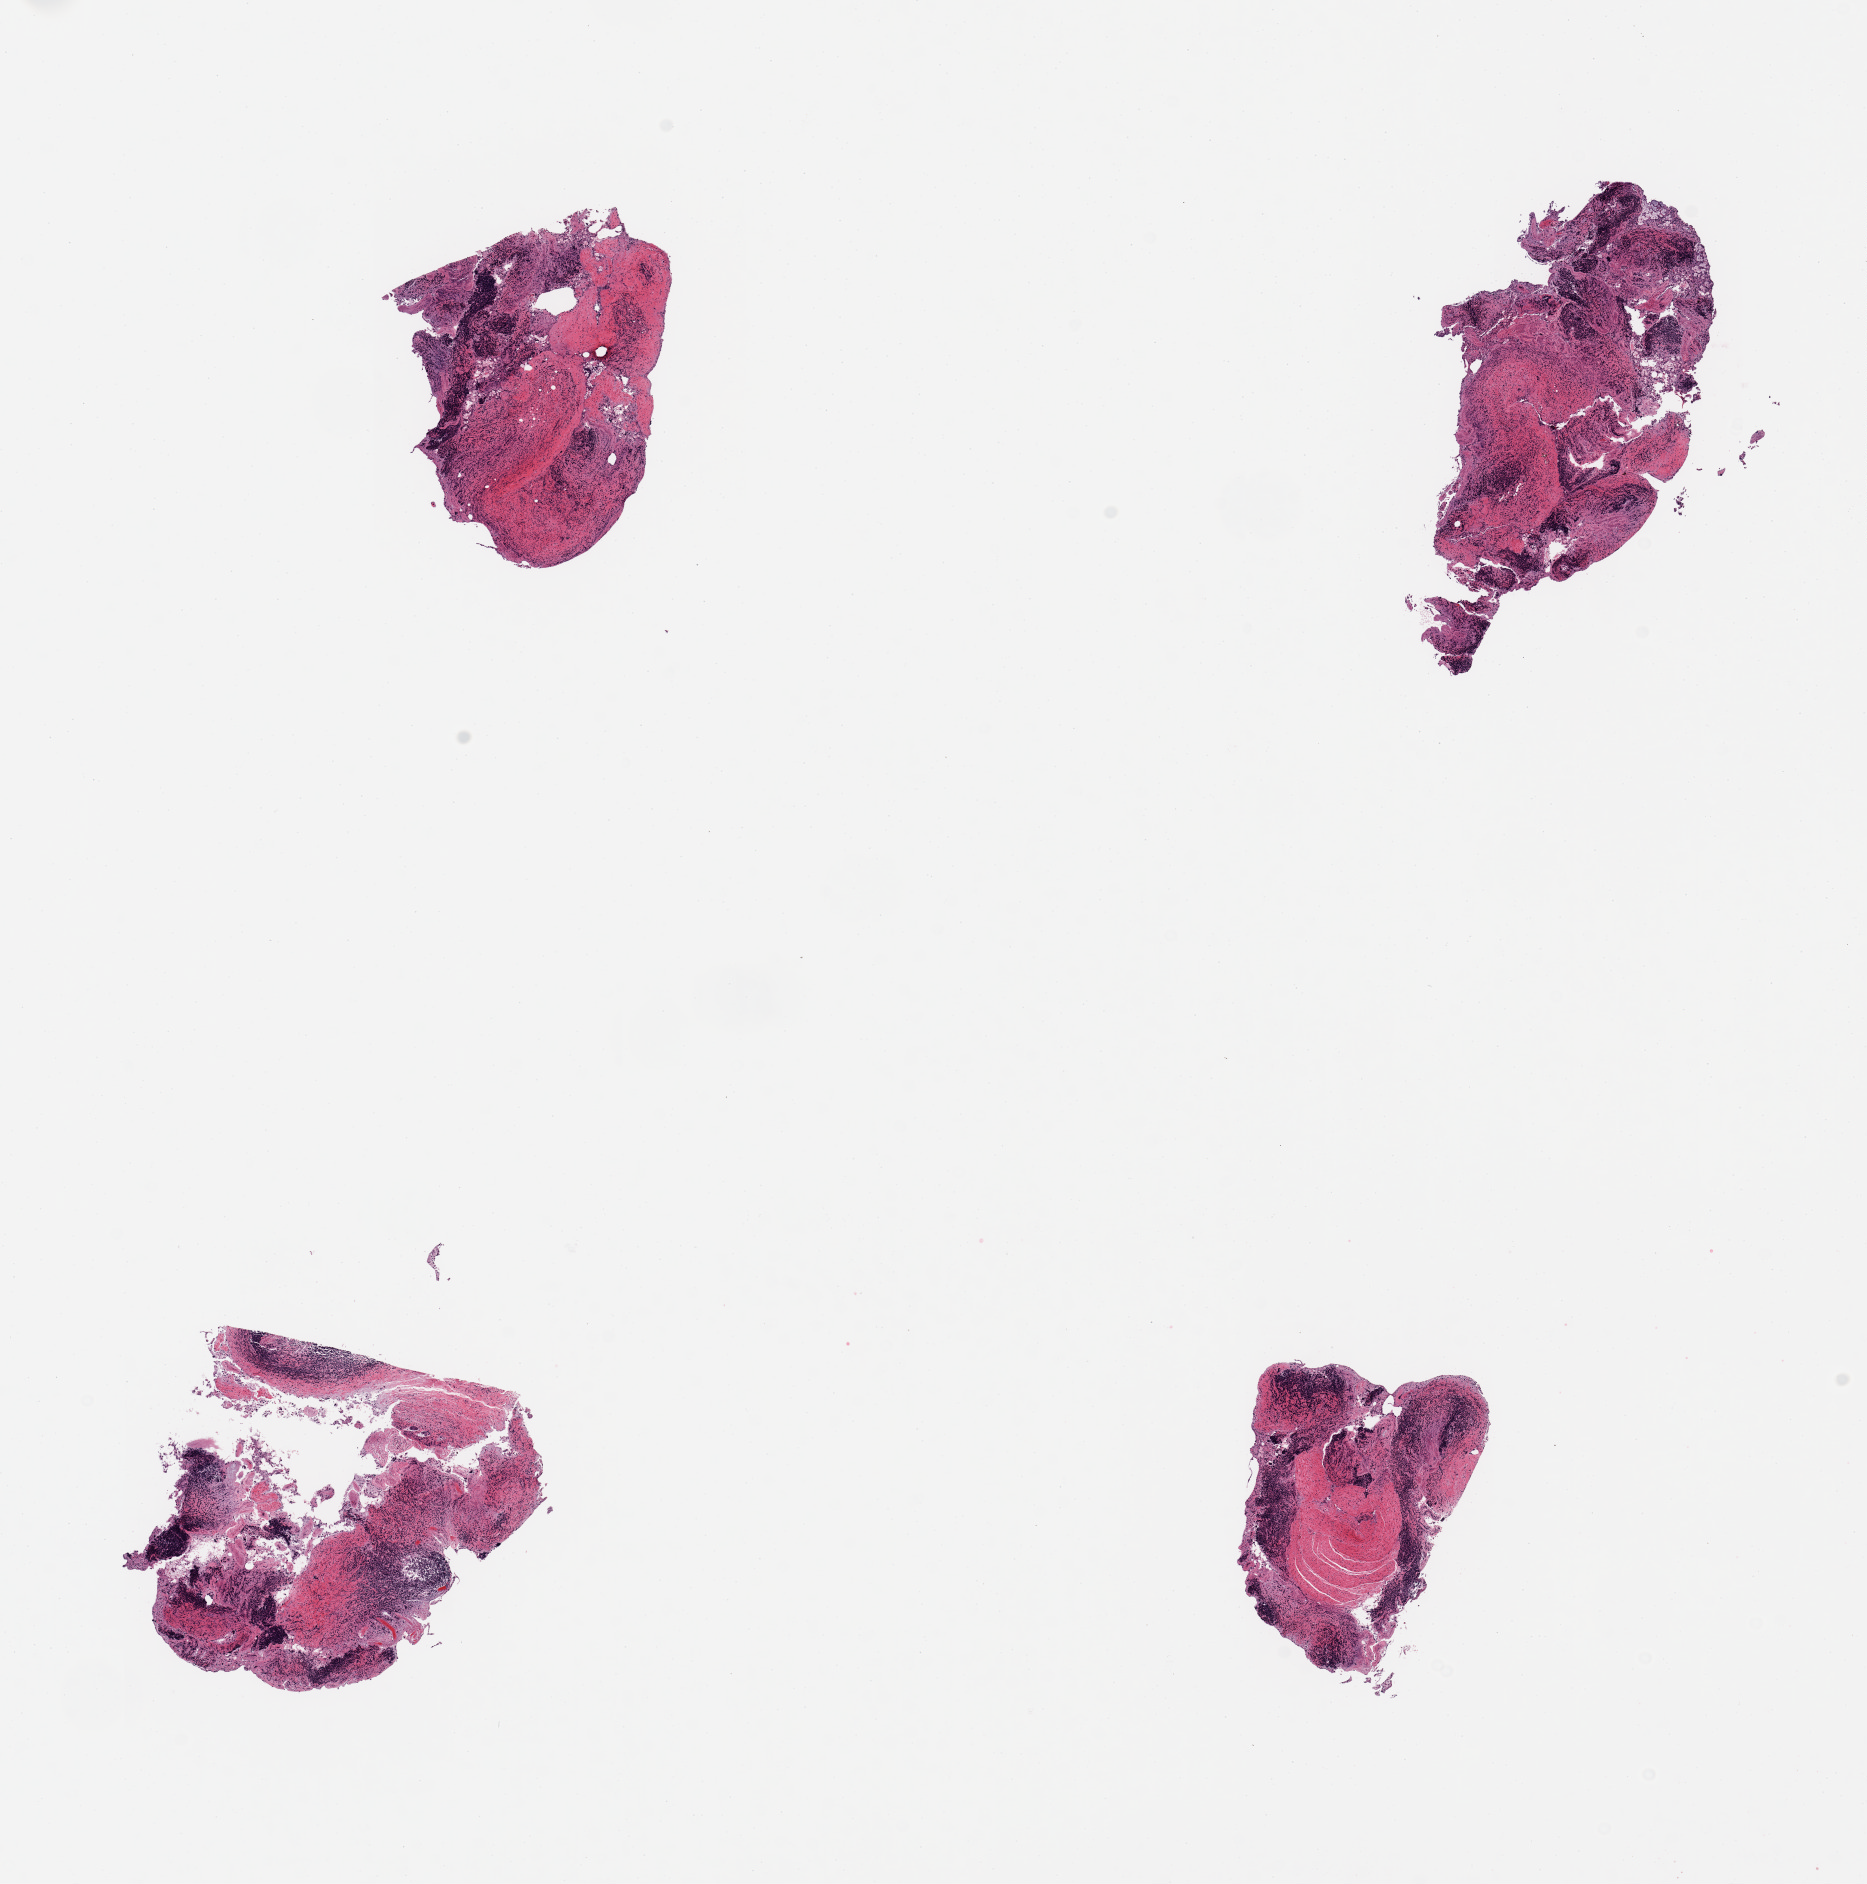
Digitized hematoxylin and eosin (H&E)-stained section, a low-resolution overview of the entire scanned area, about 14.8 x 14.9 mm (from a 20x scan). Donor sex: female.
* specimen: PAXgene-fixed, paraffin-embedded tissue; sampled site (target tissue): ileum; tissue donor sample